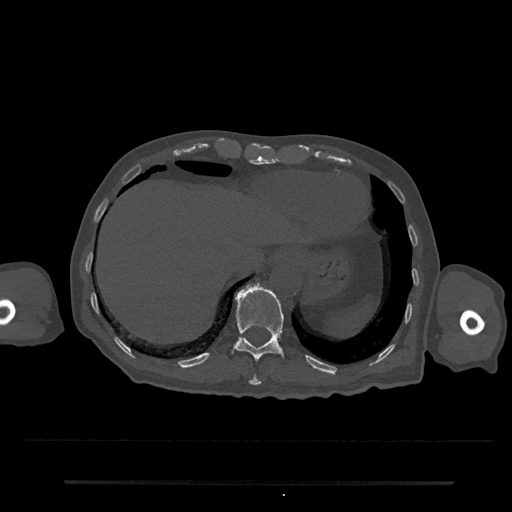
CT including the spine, one axial slice; slice 256 of 797 in the series (ordered by position); reconstruction kernel Br40s/3; 120 kVp; bone window (W 1800 / L 400 HU); 512 × 512 image matrix. Patient: male, 74 years. From the clinical record (not read from this slice): primary cancer: prostate.
Outlined on this slice (semi-automatic segmentation, software-assisted and operator-edited):
- T10 vertebra: bounding box [x1, y1, x2, y2] px = [249, 374, 261, 385]
- T11 vertebra: [231, 283, 285, 362]